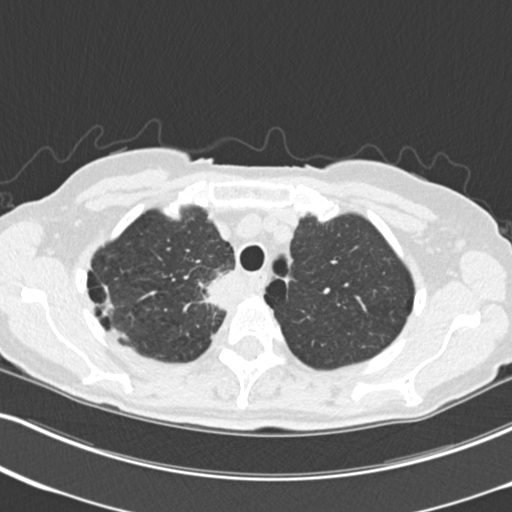
Low-dose screening chest CT, one axial slice. Slice 181 of 226 in the series (ordered by position). Reconstruction kernel B30f. Lung window (W 1500 / L -600 HU). 2 mm slice thickness. 512 × 512 image matrix, field of view 322 × 322 mm.
Outlined on this slice (outlined manually by an expert reader):
- lesion 1 (tumor, mediastinum): bounding box <203,270,236,308> (left, top, right, bottom; pixels)